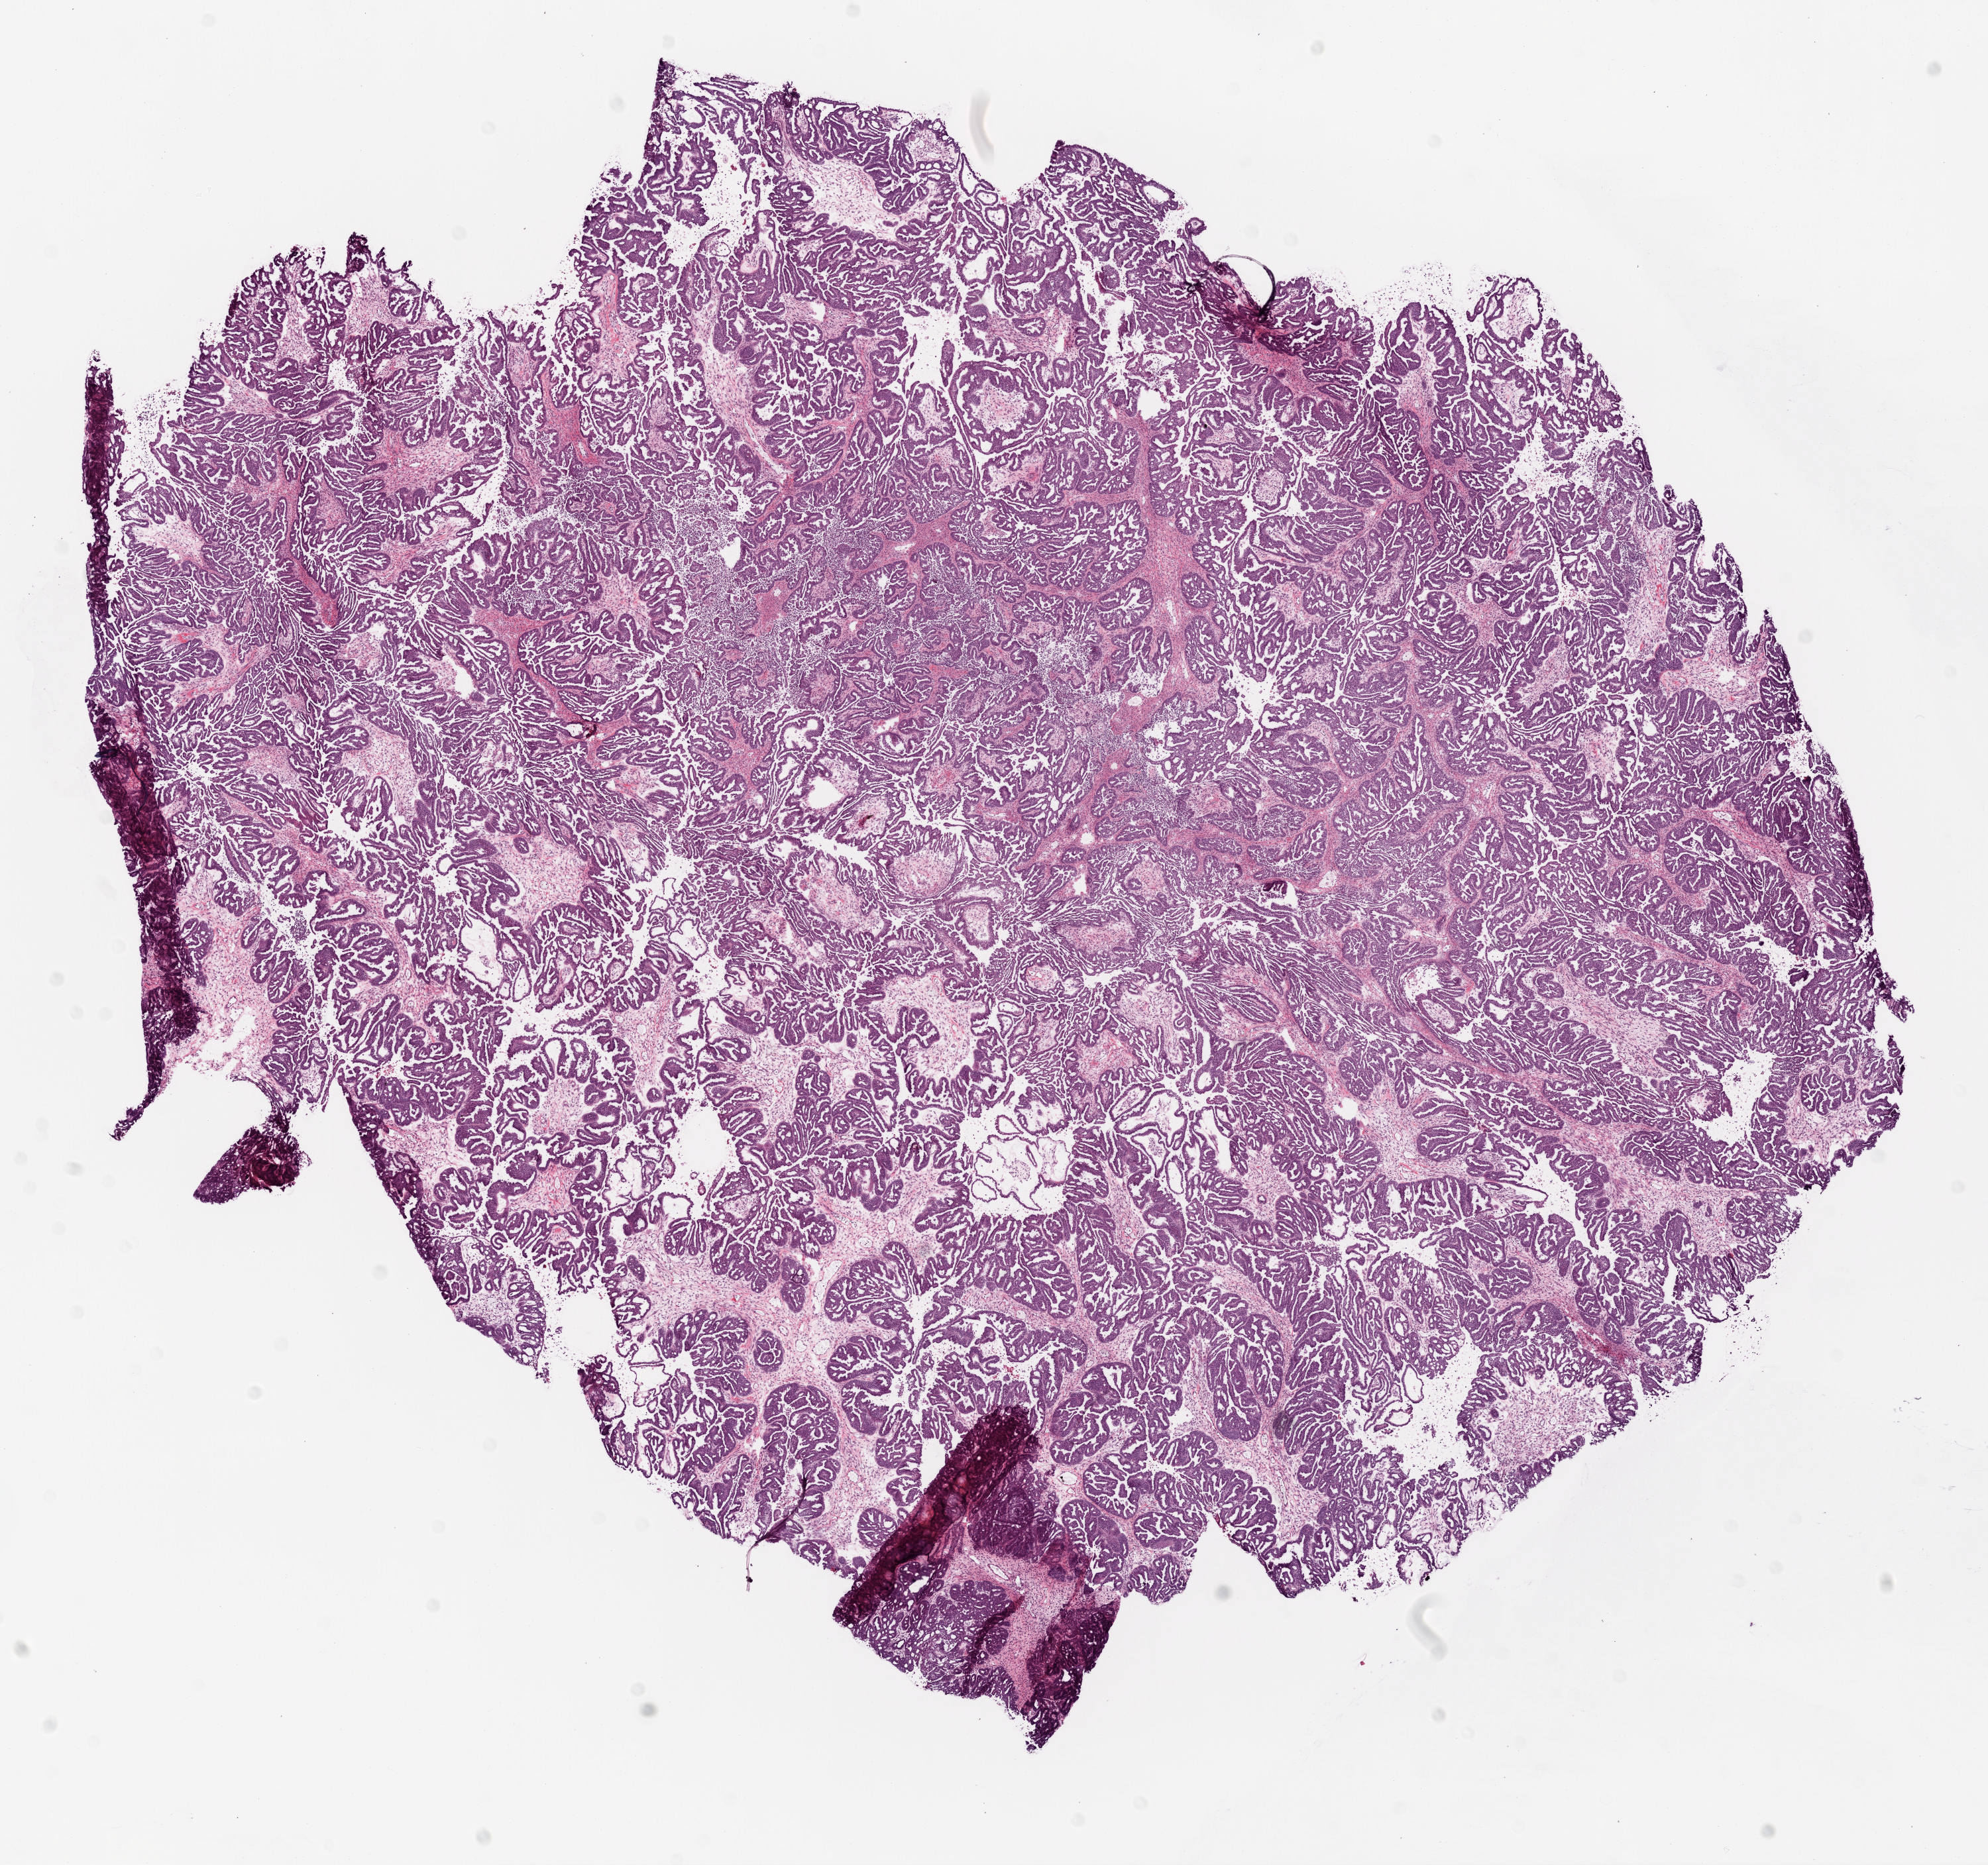
Digitized Hematoxylin and eosin (H&E) stained tissue section (whole slide), low-resolution overview of the scanned area, about 12.0 x 11.3 mm (slide scanned at 20x); frozen section; ovary, primary tumour sample. Patient: female, age at initial diagnosis 37 years. Histologic grade: G1 (well differentiated). Composition of this section per pathologist review: tumour cells 85%, tumour nuclei 90%, normal cells 5%, stromal cells 8%, necrosis 2%.
FIGO stage: IIIC. Laterality: bilateral. Diagnosis: Serous cystadenocarcinoma, NOS.